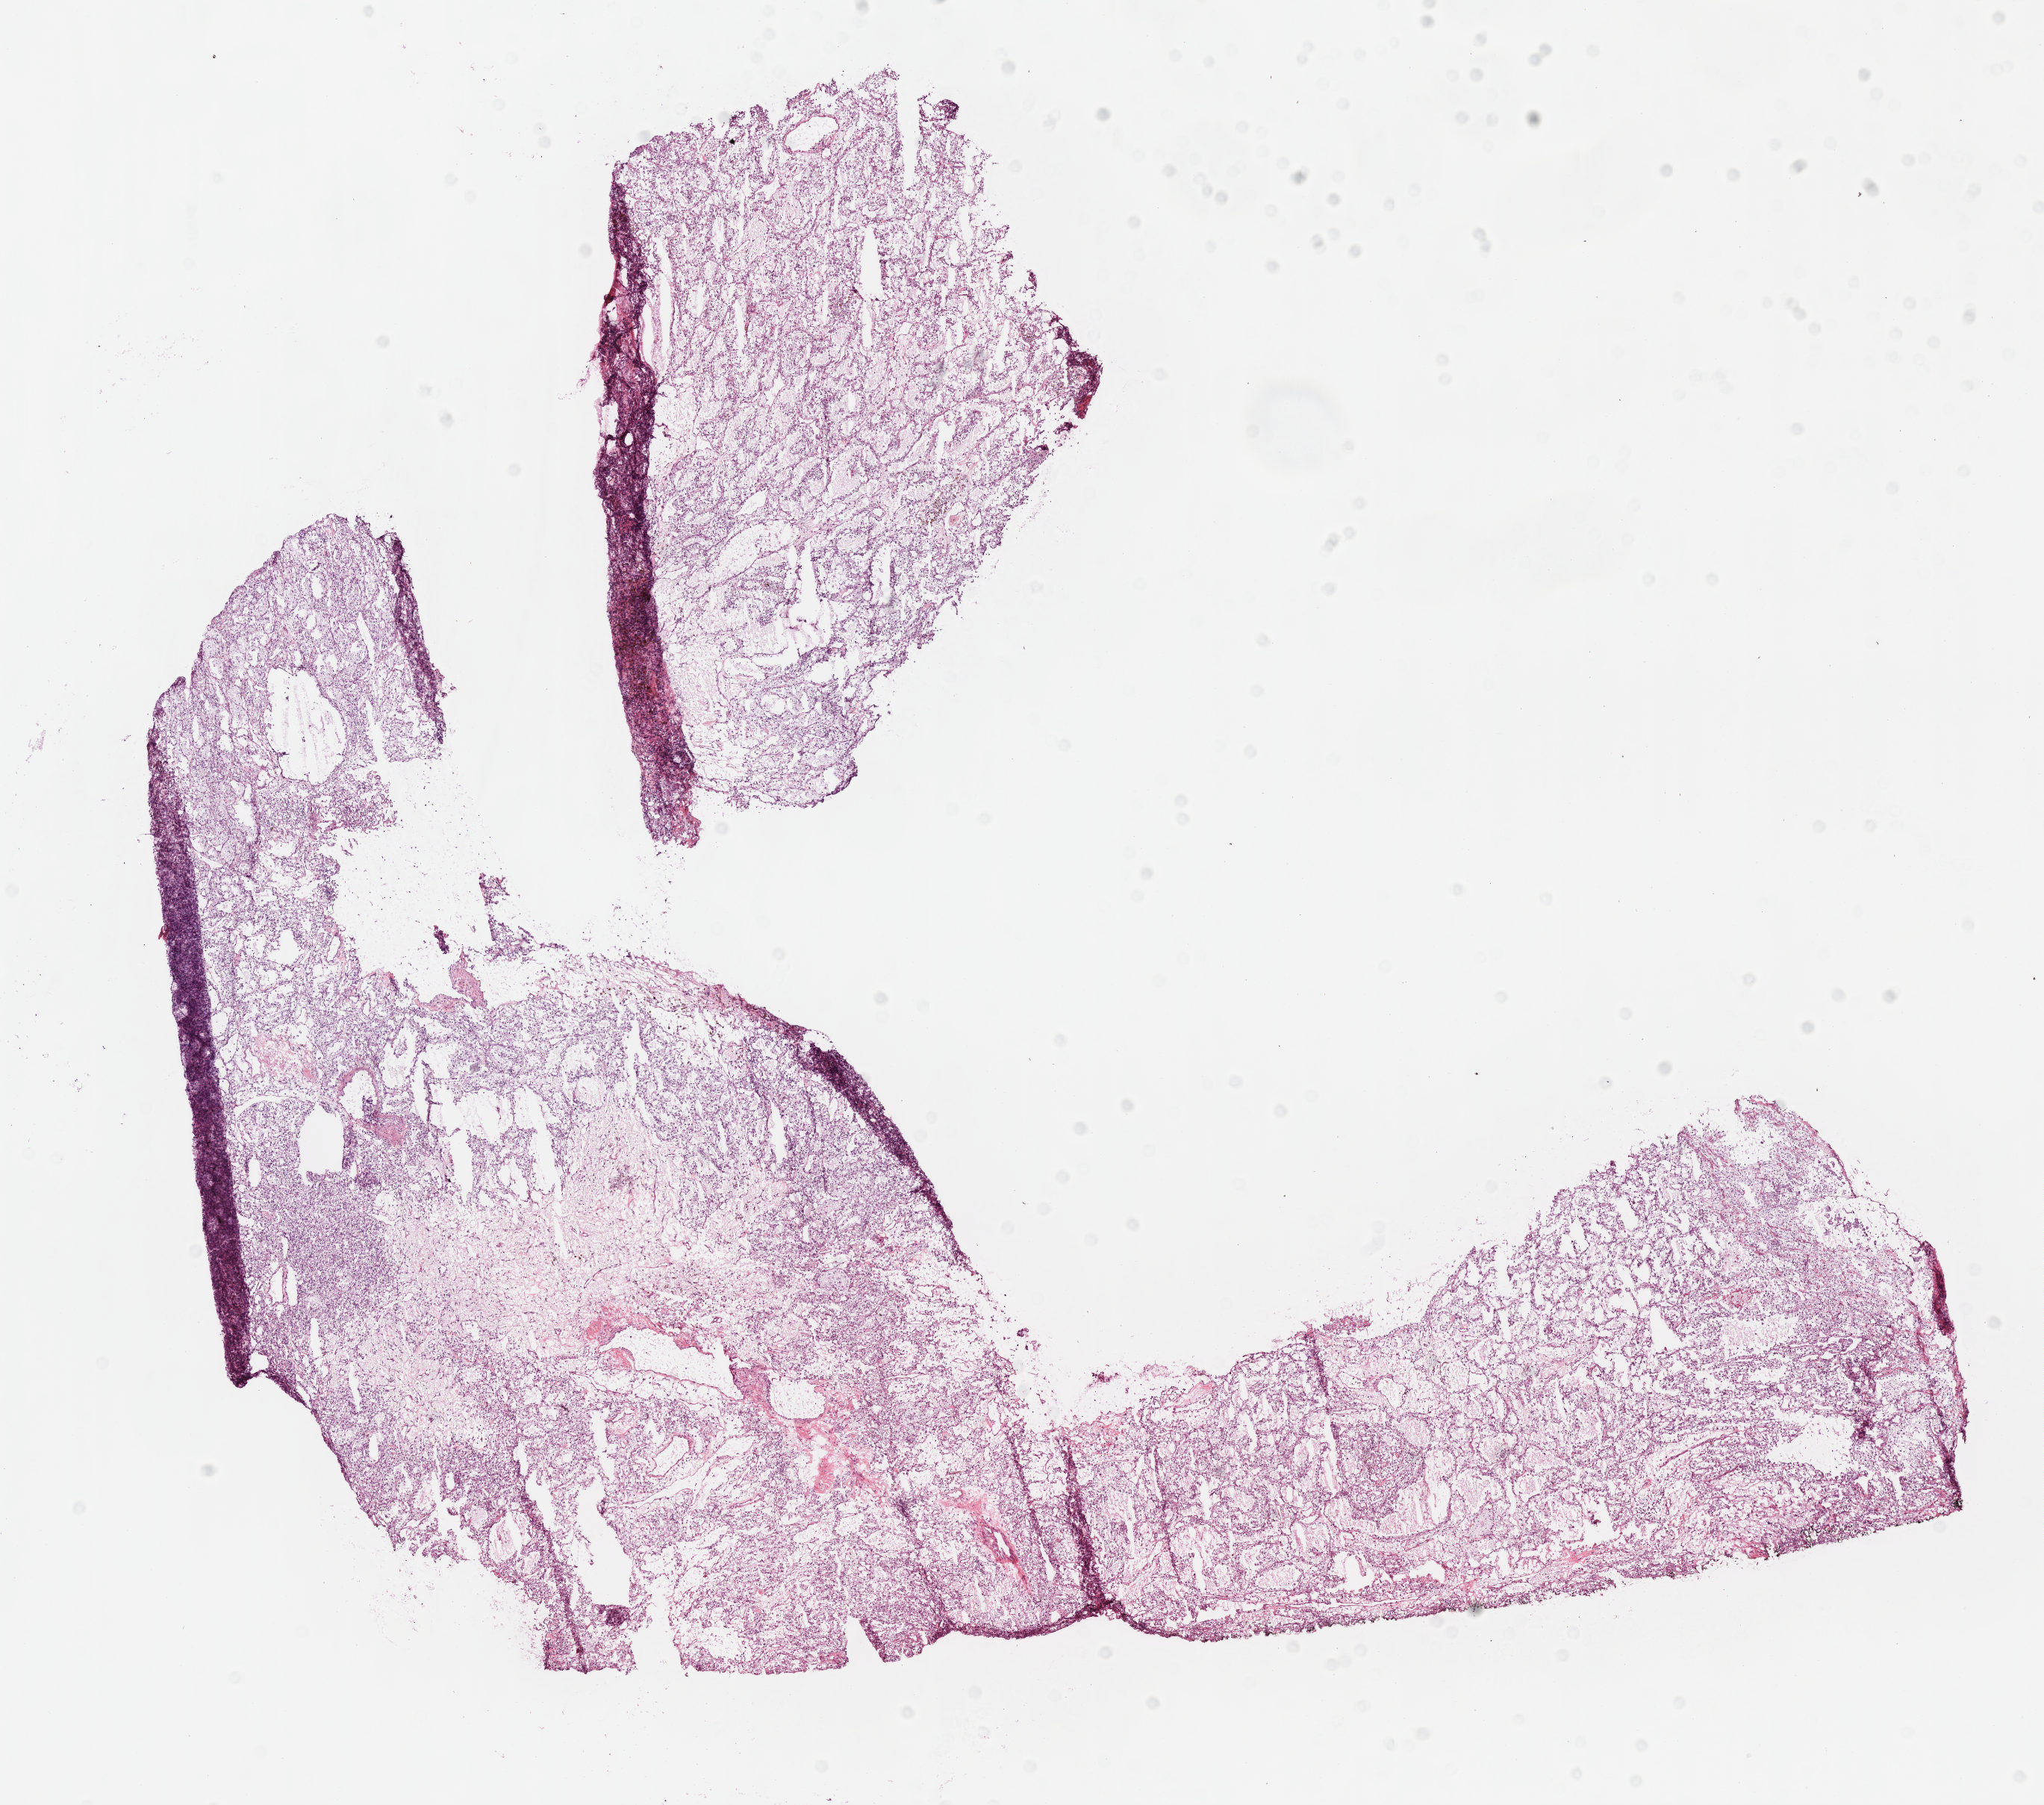
Digitized H&E tissue section (whole slide), a low-resolution overview of the entire scanned area, about 11.1 x 9.8 mm (slide scanned at 40x); frozen section; primary tumour sample from the kidney. Patient: male, age at initial diagnosis 56 years. Histologic grade: G2 (moderately differentiated). Slide review estimates, as recorded: tumour cells 95%, tumour nuclei 80%, normal cells 0%, stromal cells 5%, necrosis 0%.
Histologic diagnosis: Clear cell adenocarcinoma, NOS. AJCC pathologic stage: I.